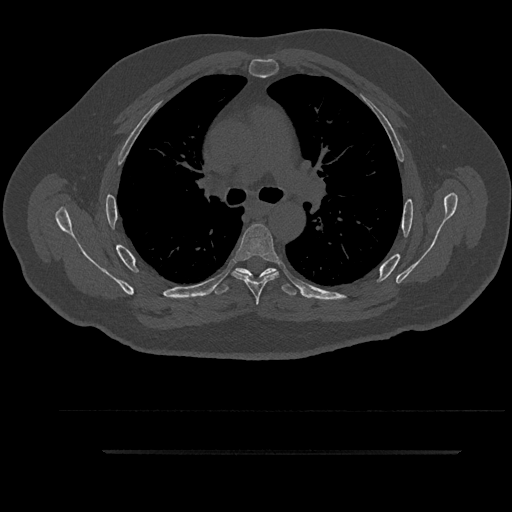
CT including the spine, one axial slice. Slice 615 of 797 in the series (ordered by position). 120 kVp. Bone window (W 1800 / L 400 HU). 0.5 mm slice thickness. 512 × 512 image matrix, field of view 432 × 432 mm. Male patient, age 63 years. From the clinical record (not read from this slice): primary cancer: renal.
Annotated regions visible in this slice (semi-automatically segmented with operator editing):
- T5 vertebra: bounding box [x1, y1, x2, y2] px = [232, 224, 280, 305]
- T6 vertebra: [212, 268, 297, 295]